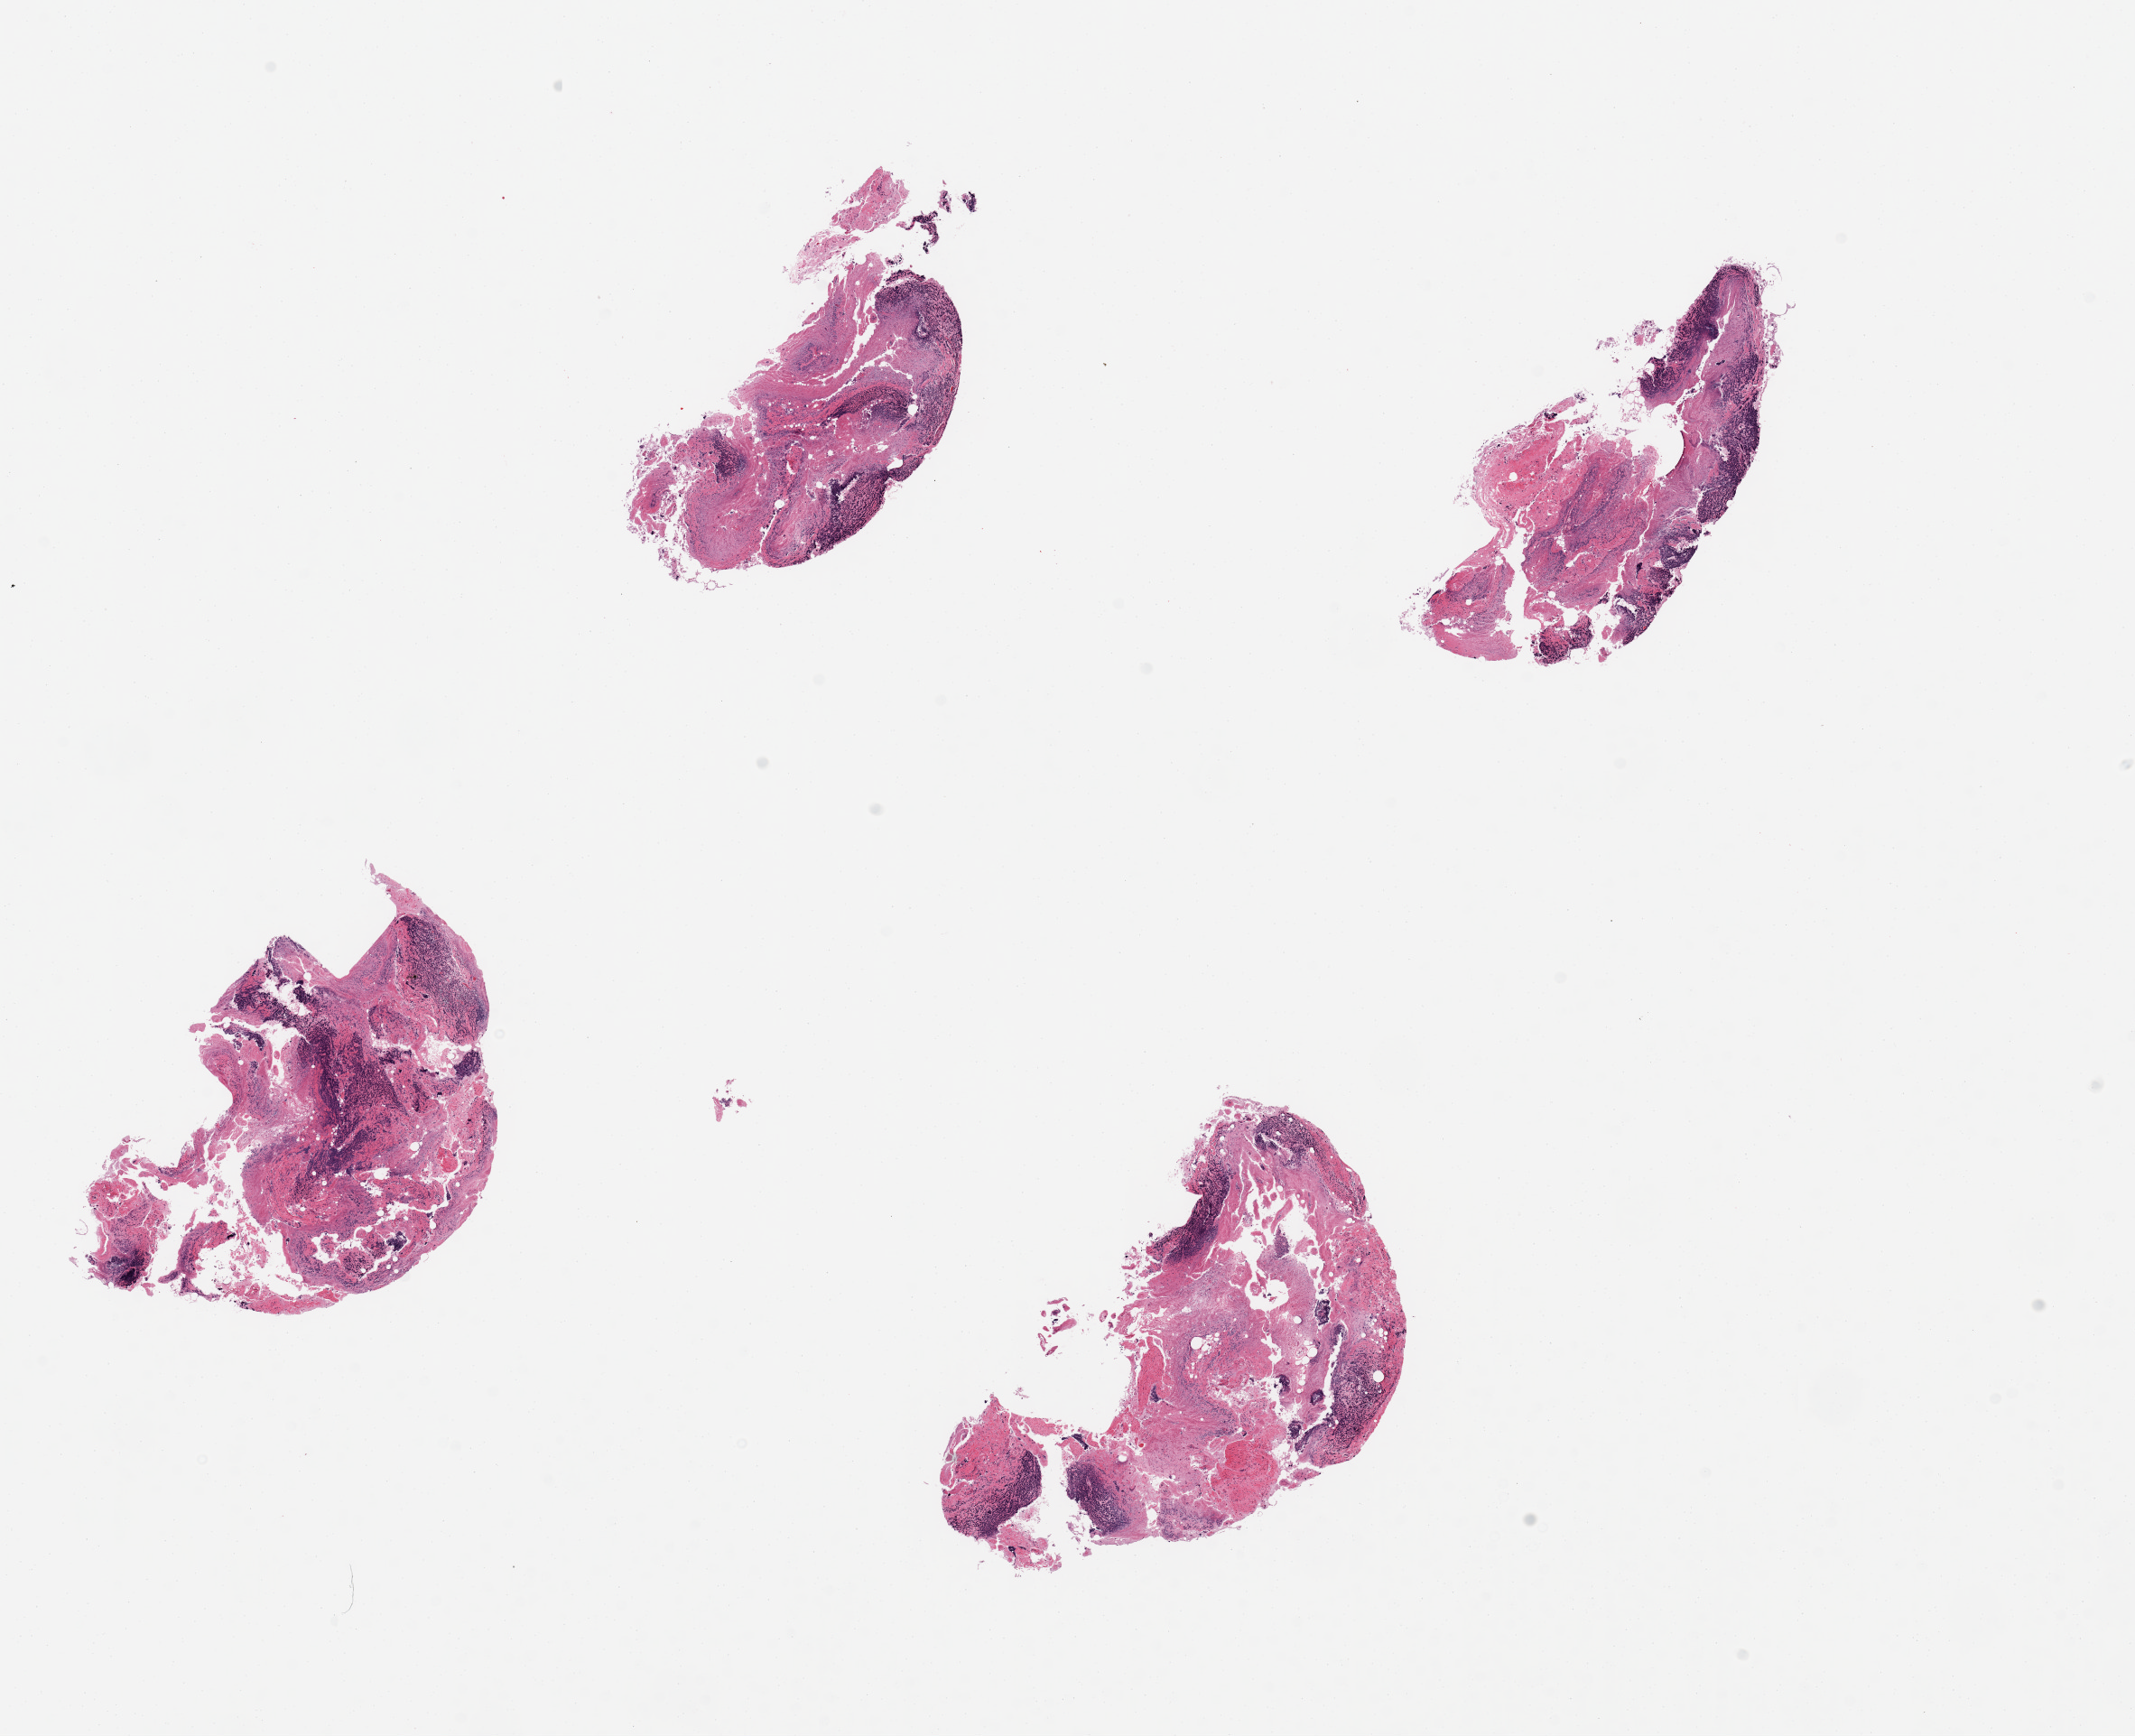
Whole-slide image, hematoxylin and eosin (H&E) stain — low-resolution overview of the scanned area, about 18.7 x 15.2 mm (from a 20x scan). PAXgene-fixed paraffin-embedded (PFPE) section. Section of ileum (target tissue). Donor tissue sample.
Pathologist's review note for this sample: 4 pieces; good lymphoid component, but severe autolysis, small portion of muscularis (not target).